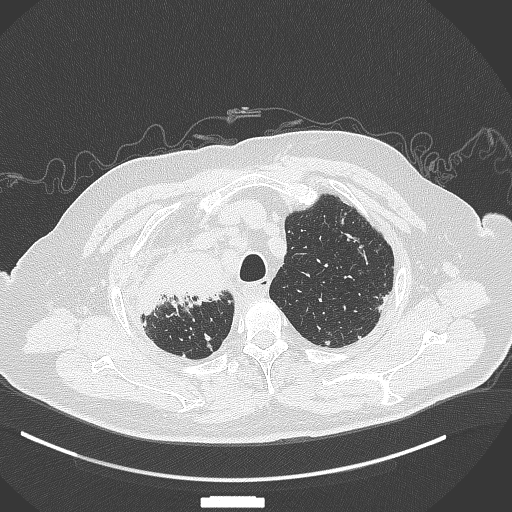
Chest CT, one axial slice; slice 302 of 384 in the series (ordered by position); lung window (W 1500 / L -600 HU); 1 mm slice thickness; 512 × 512 image matrix. Patient: male, 69 years. Case-level facts recorded for this patient, not image findings: clinical TNM (as recorded): T4 N3 M1.
Annotated regions visible in this slice (bounding box drawn by a radiologist):
- lung tumour (recorded histology: adenocarcinoma): bounding box <134,246,230,318> (left, top, right, bottom; pixels)